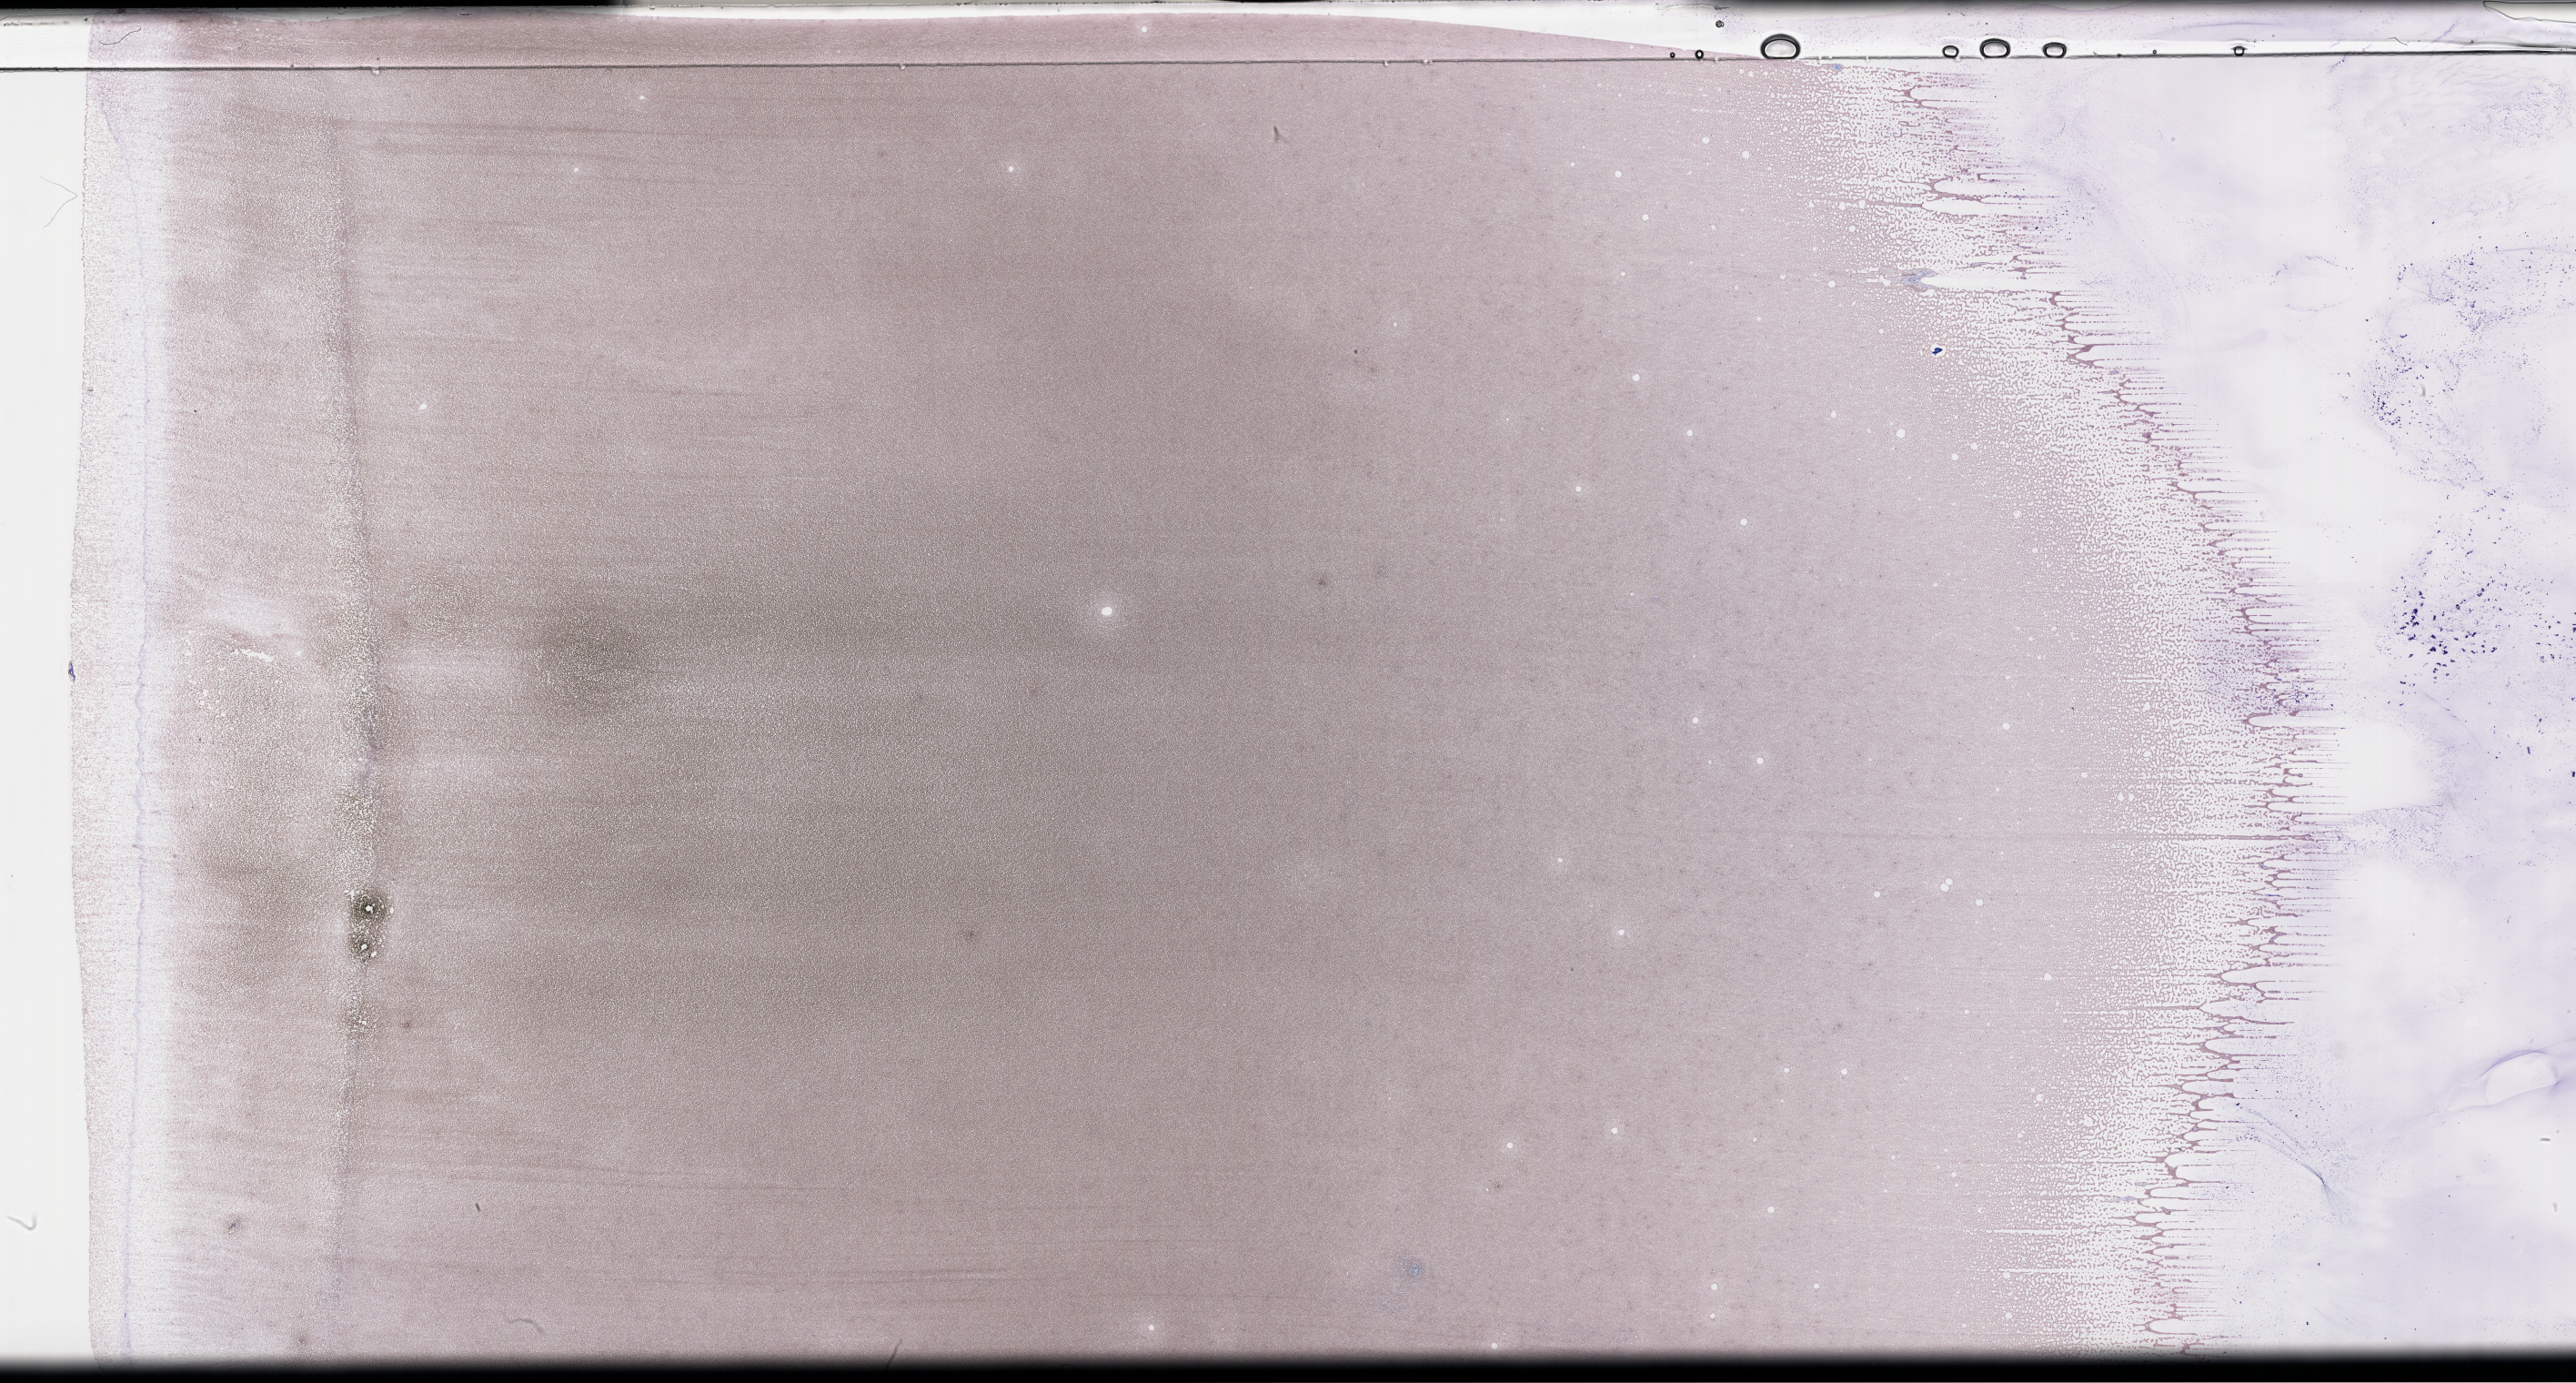
Wright-Giemsa-stained whole blood smear, whole-slide image — a low-resolution overview of the entire scanned area, about 45.7 x 24.5 mm. Smear from an EDTA sample. Specimen time point: collected on treatment. Patient sex: female.
- from a patient with: Plasma Cell Myeloma